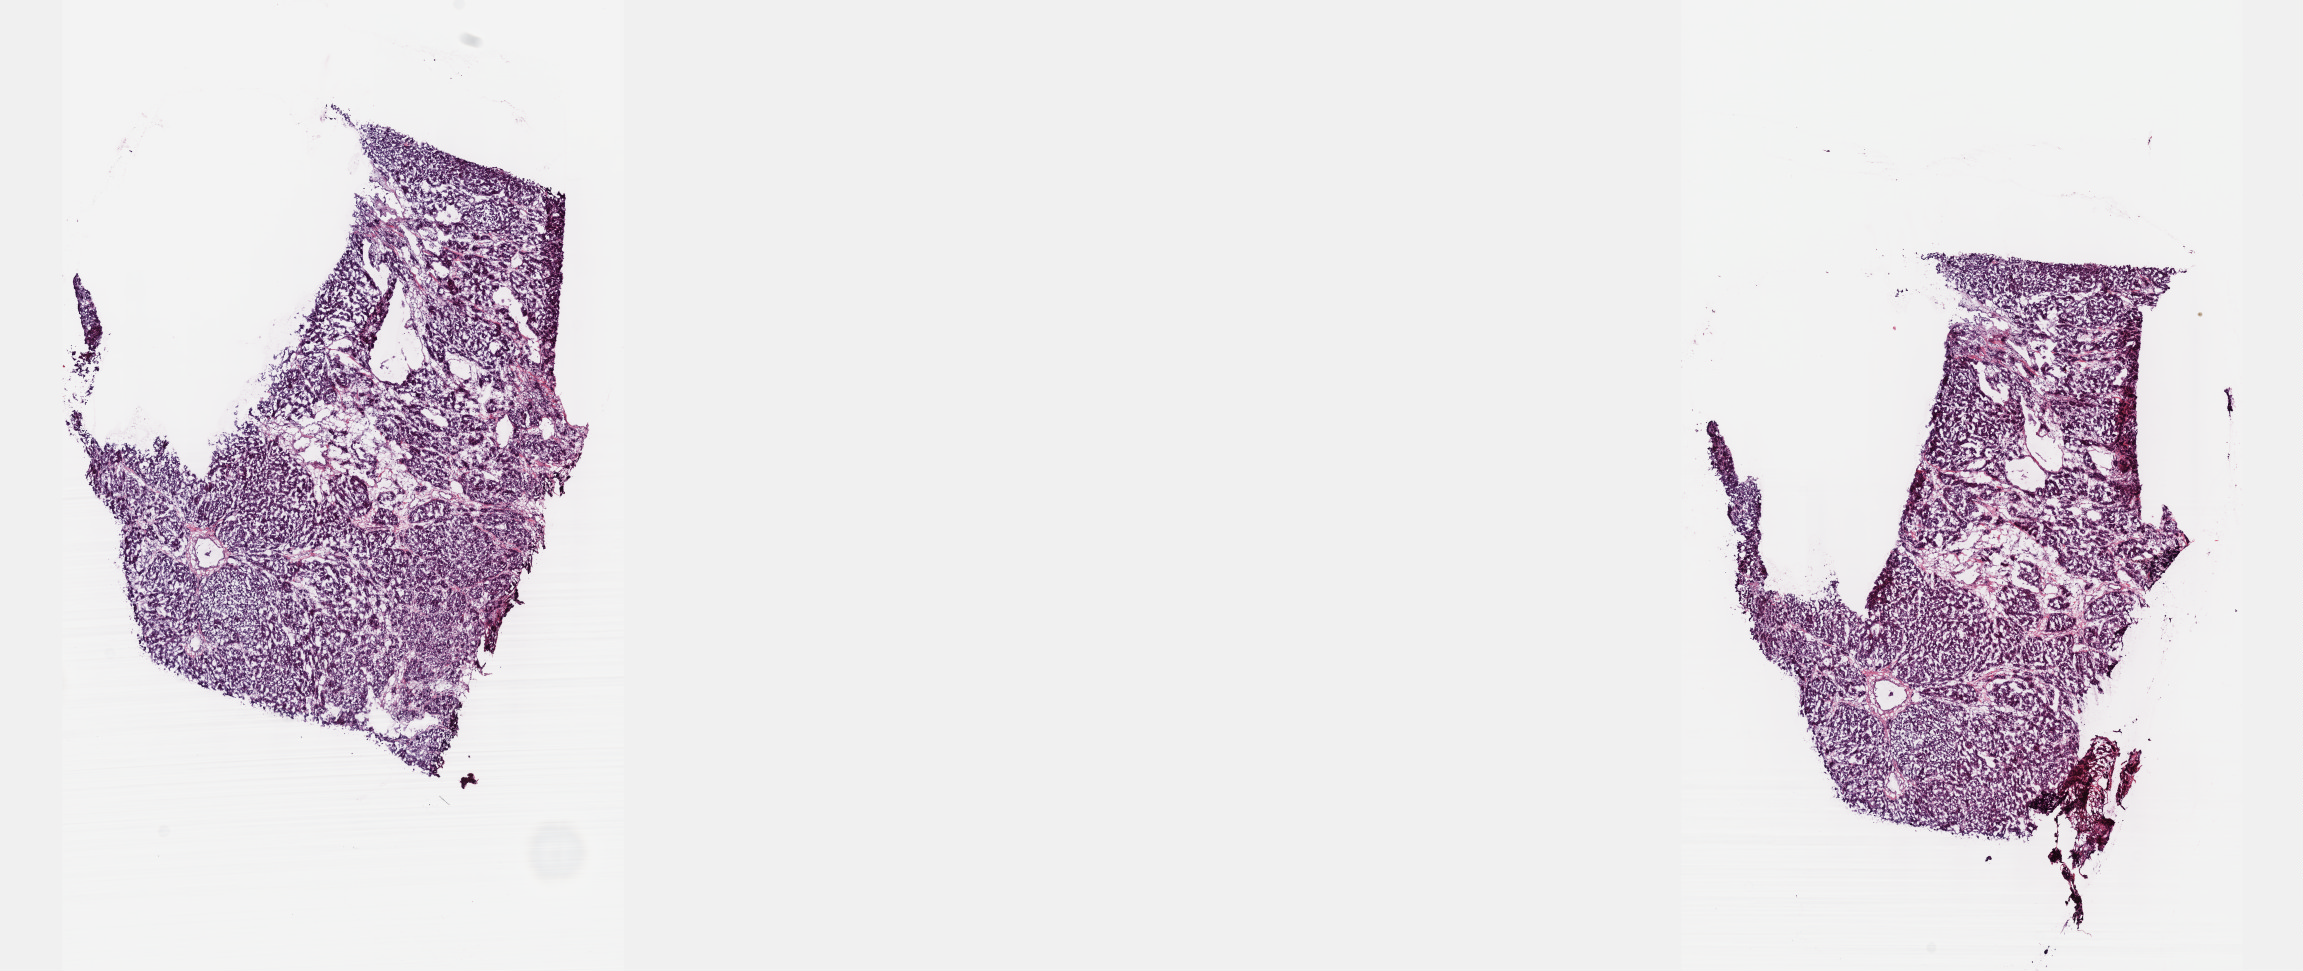
Digitized H&E tissue section (whole slide) — low-resolution overview of the scanned area, about 18.6 x 7.8 mm (acquisition: 40x scan), frozen section from the top of the tissue portion, primary tumour sample from the liver. Patient: male, age at initial diagnosis 59 years. Histologic grade: G1 (well differentiated). Slide review estimates, as recorded: tumour cells 100%, tumour nuclei 80%, normal cells 0%, stromal cells 0%, necrosis 0%. Infiltration values recorded for this section: lymphocyte infiltration 2%, monocyte infiltration 0%, neutrophil infiltration 0%.
• AJCC pathologic stage: IIIA (6th edition)
• TNM: T3 N0 M0
• diagnosis: Hepatocellular carcinoma, NOS